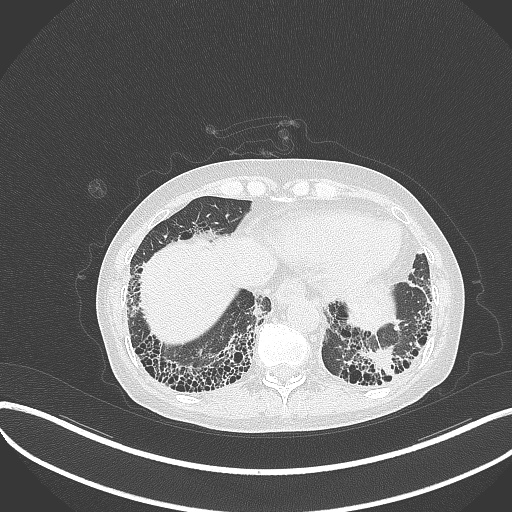
Chest CT, one axial slice. Slice 64 of 373 in the series (ordered by position). Reconstruction kernel B70f. Lung window (W 1500 / L -600 HU). 1 mm slice thickness. 512 × 512 image matrix, field of view 400 × 400 mm. Patient: female, 56 years. From the clinical record (not read from this slice): clinical TNM (as recorded): T1 N0 M0.
Annotated regions visible in this slice (rectangle marked by the reading radiologist):
- lung tumour (recorded histology: adenocarcinoma): bounding box (x1, y1, x2, y2) in pixels: (357, 343, 399, 378)